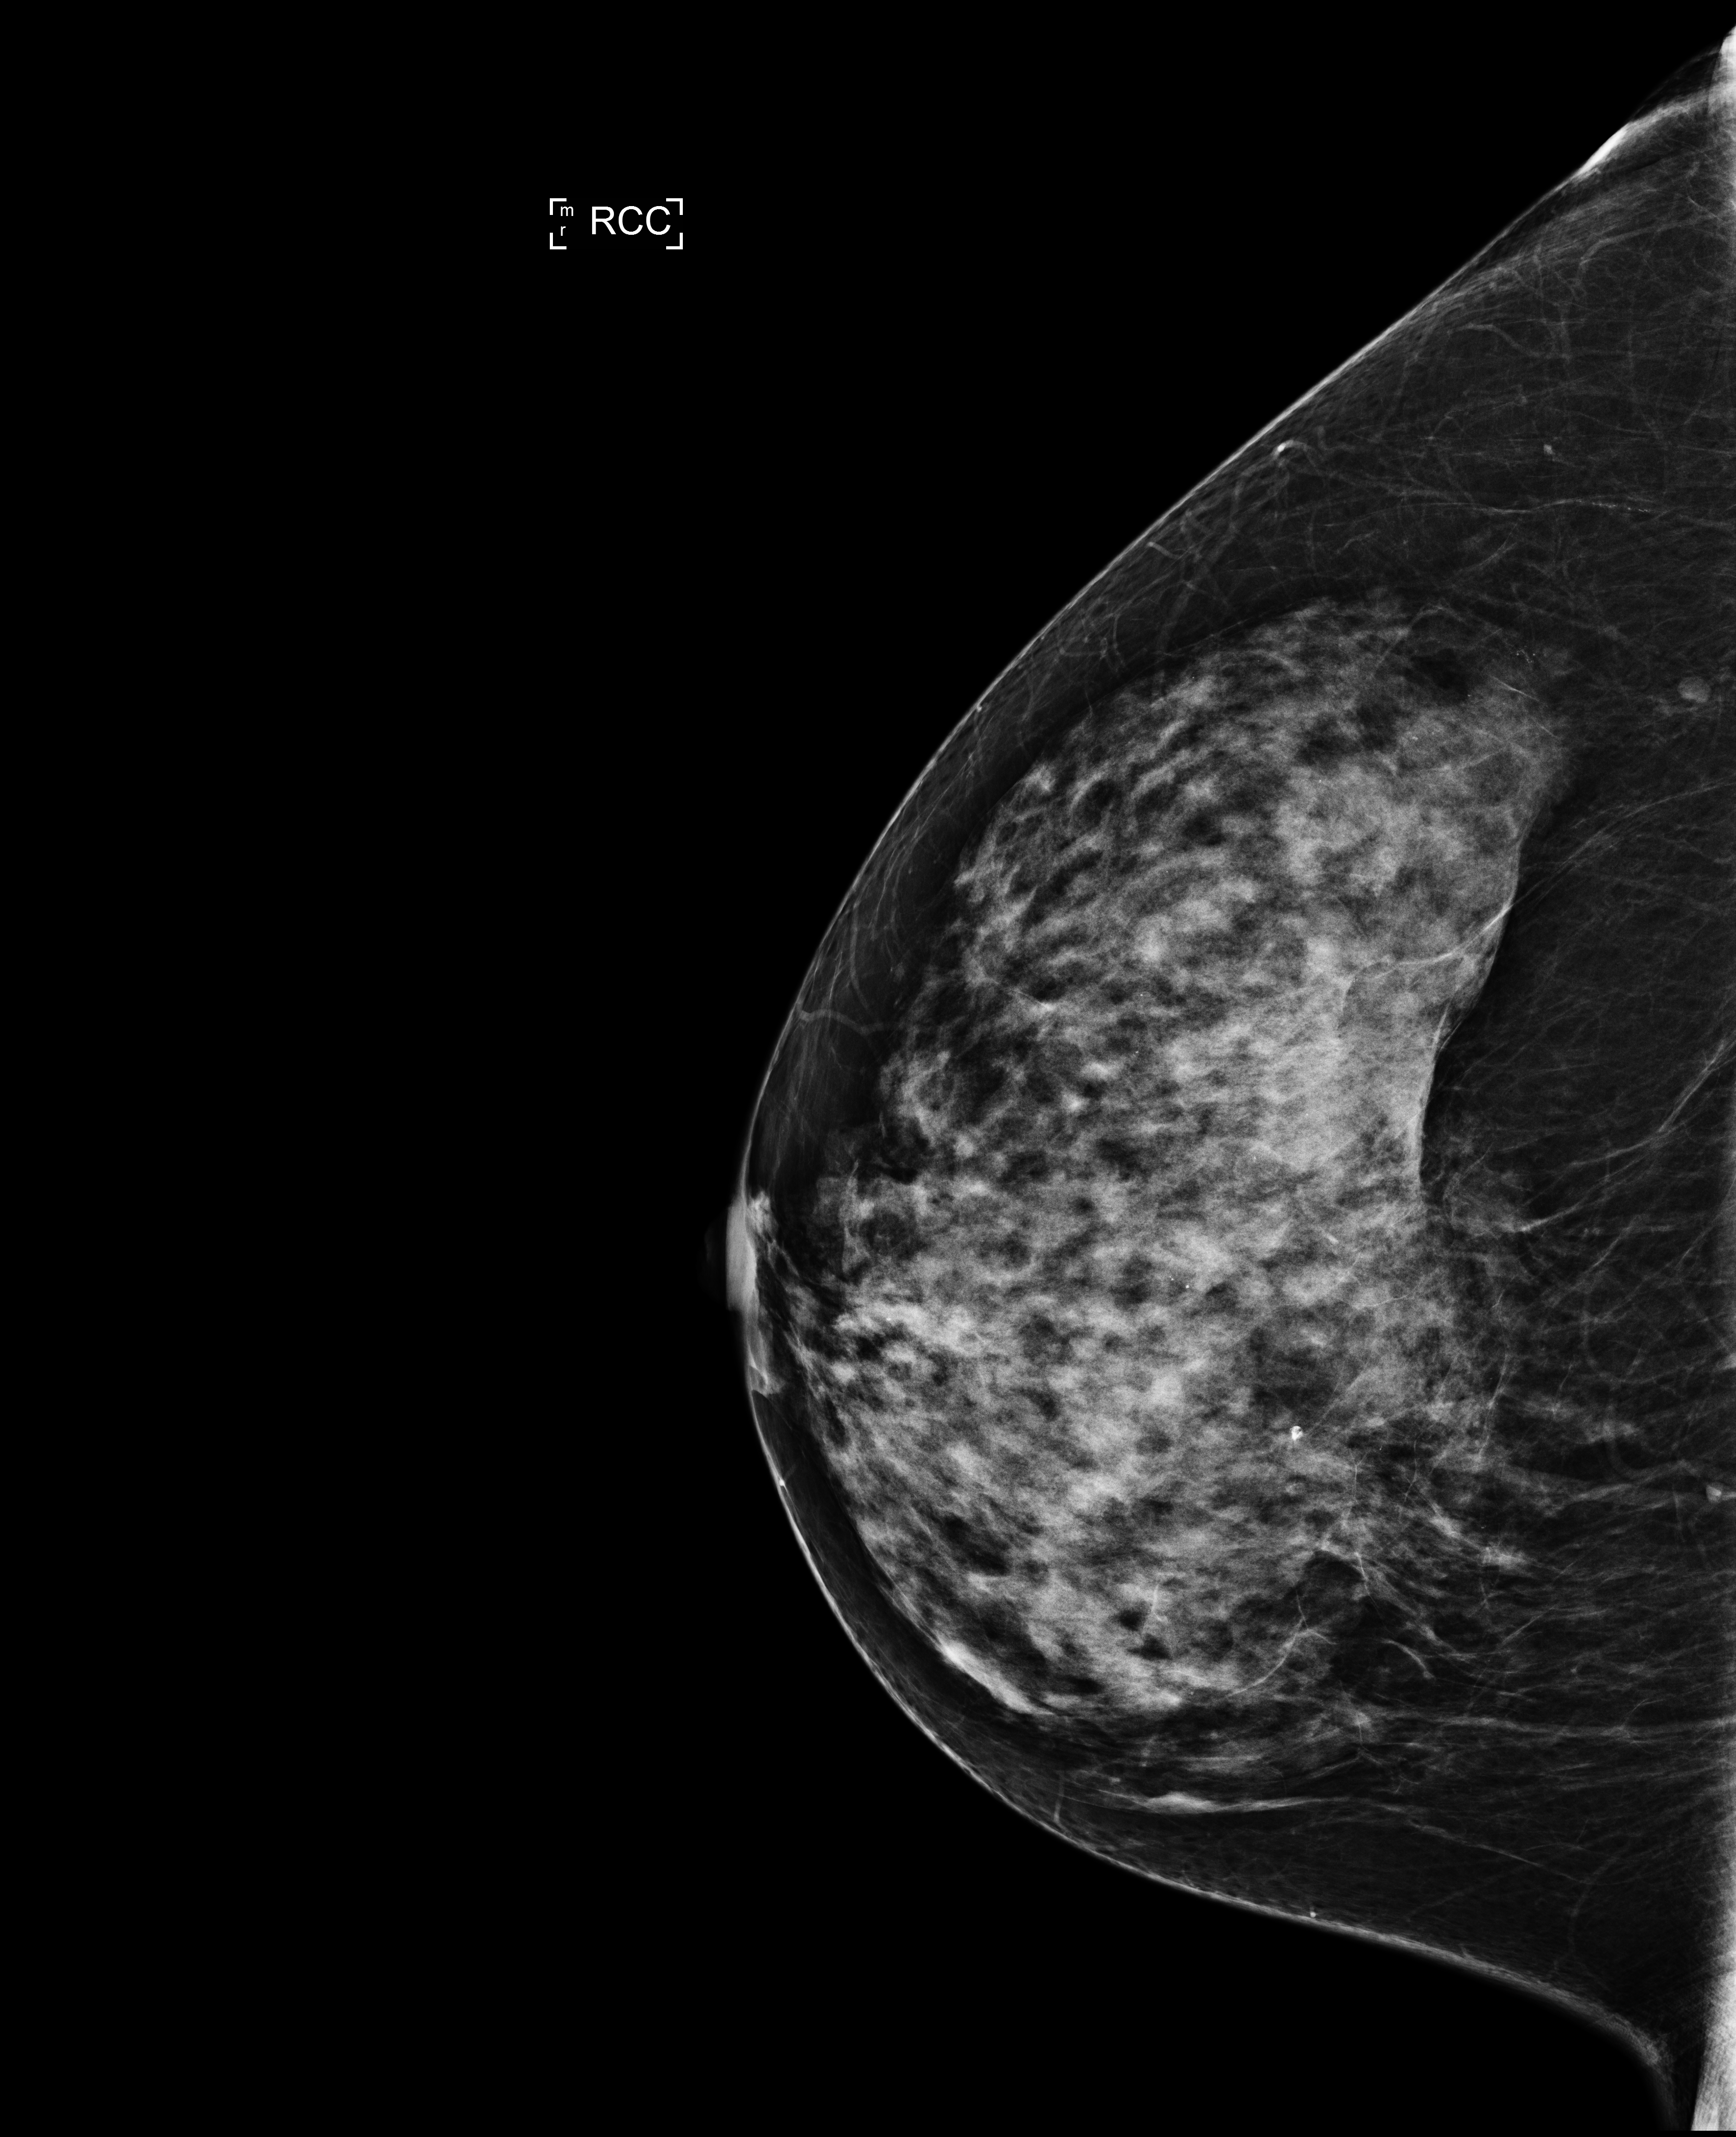
Screening examination. Patient: female, 57 years.
Image type: full-field digital mammogram. Breast: right. Projection: craniocaudal (CC) view.